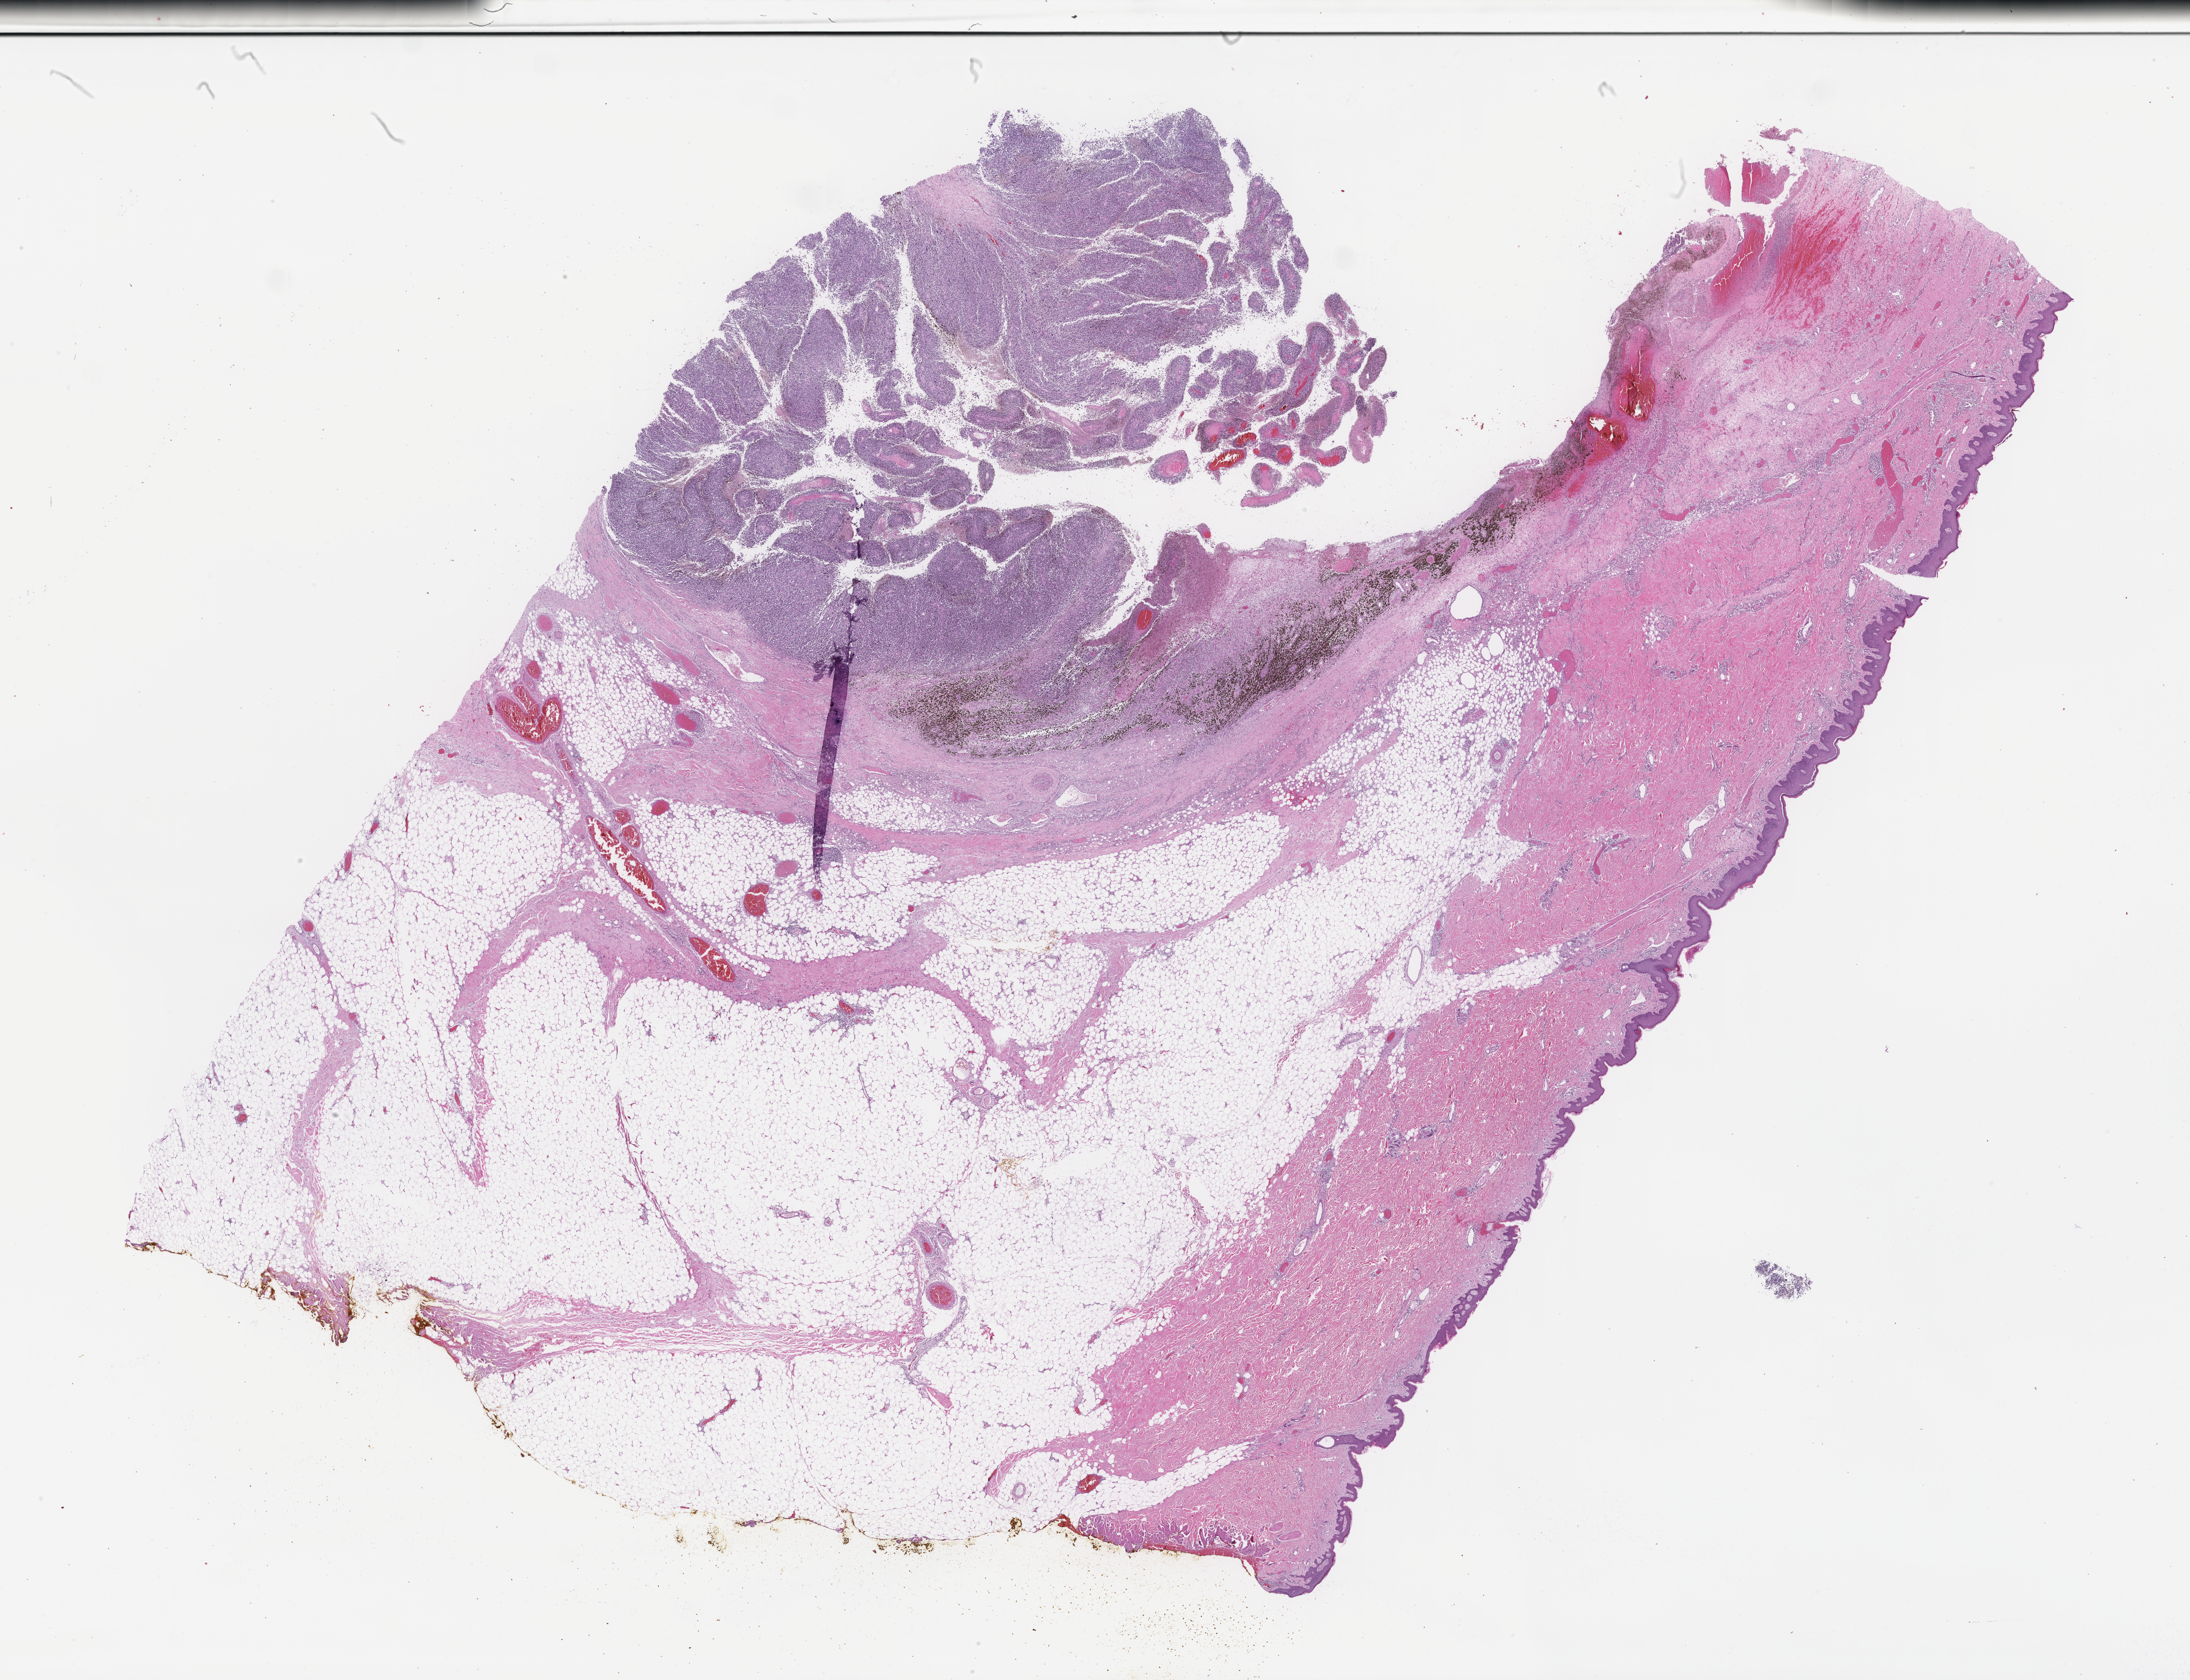
Haematoxylin and eosin whole-slide image, low-resolution overview of the scanned area, about 30.7 x 23.5 mm, formalin-fixed paraffin-embedded section. Patient sex: female.
This section: metastasis (sampled organ not recorded). Primary diagnosis of the patient: Melanoma.